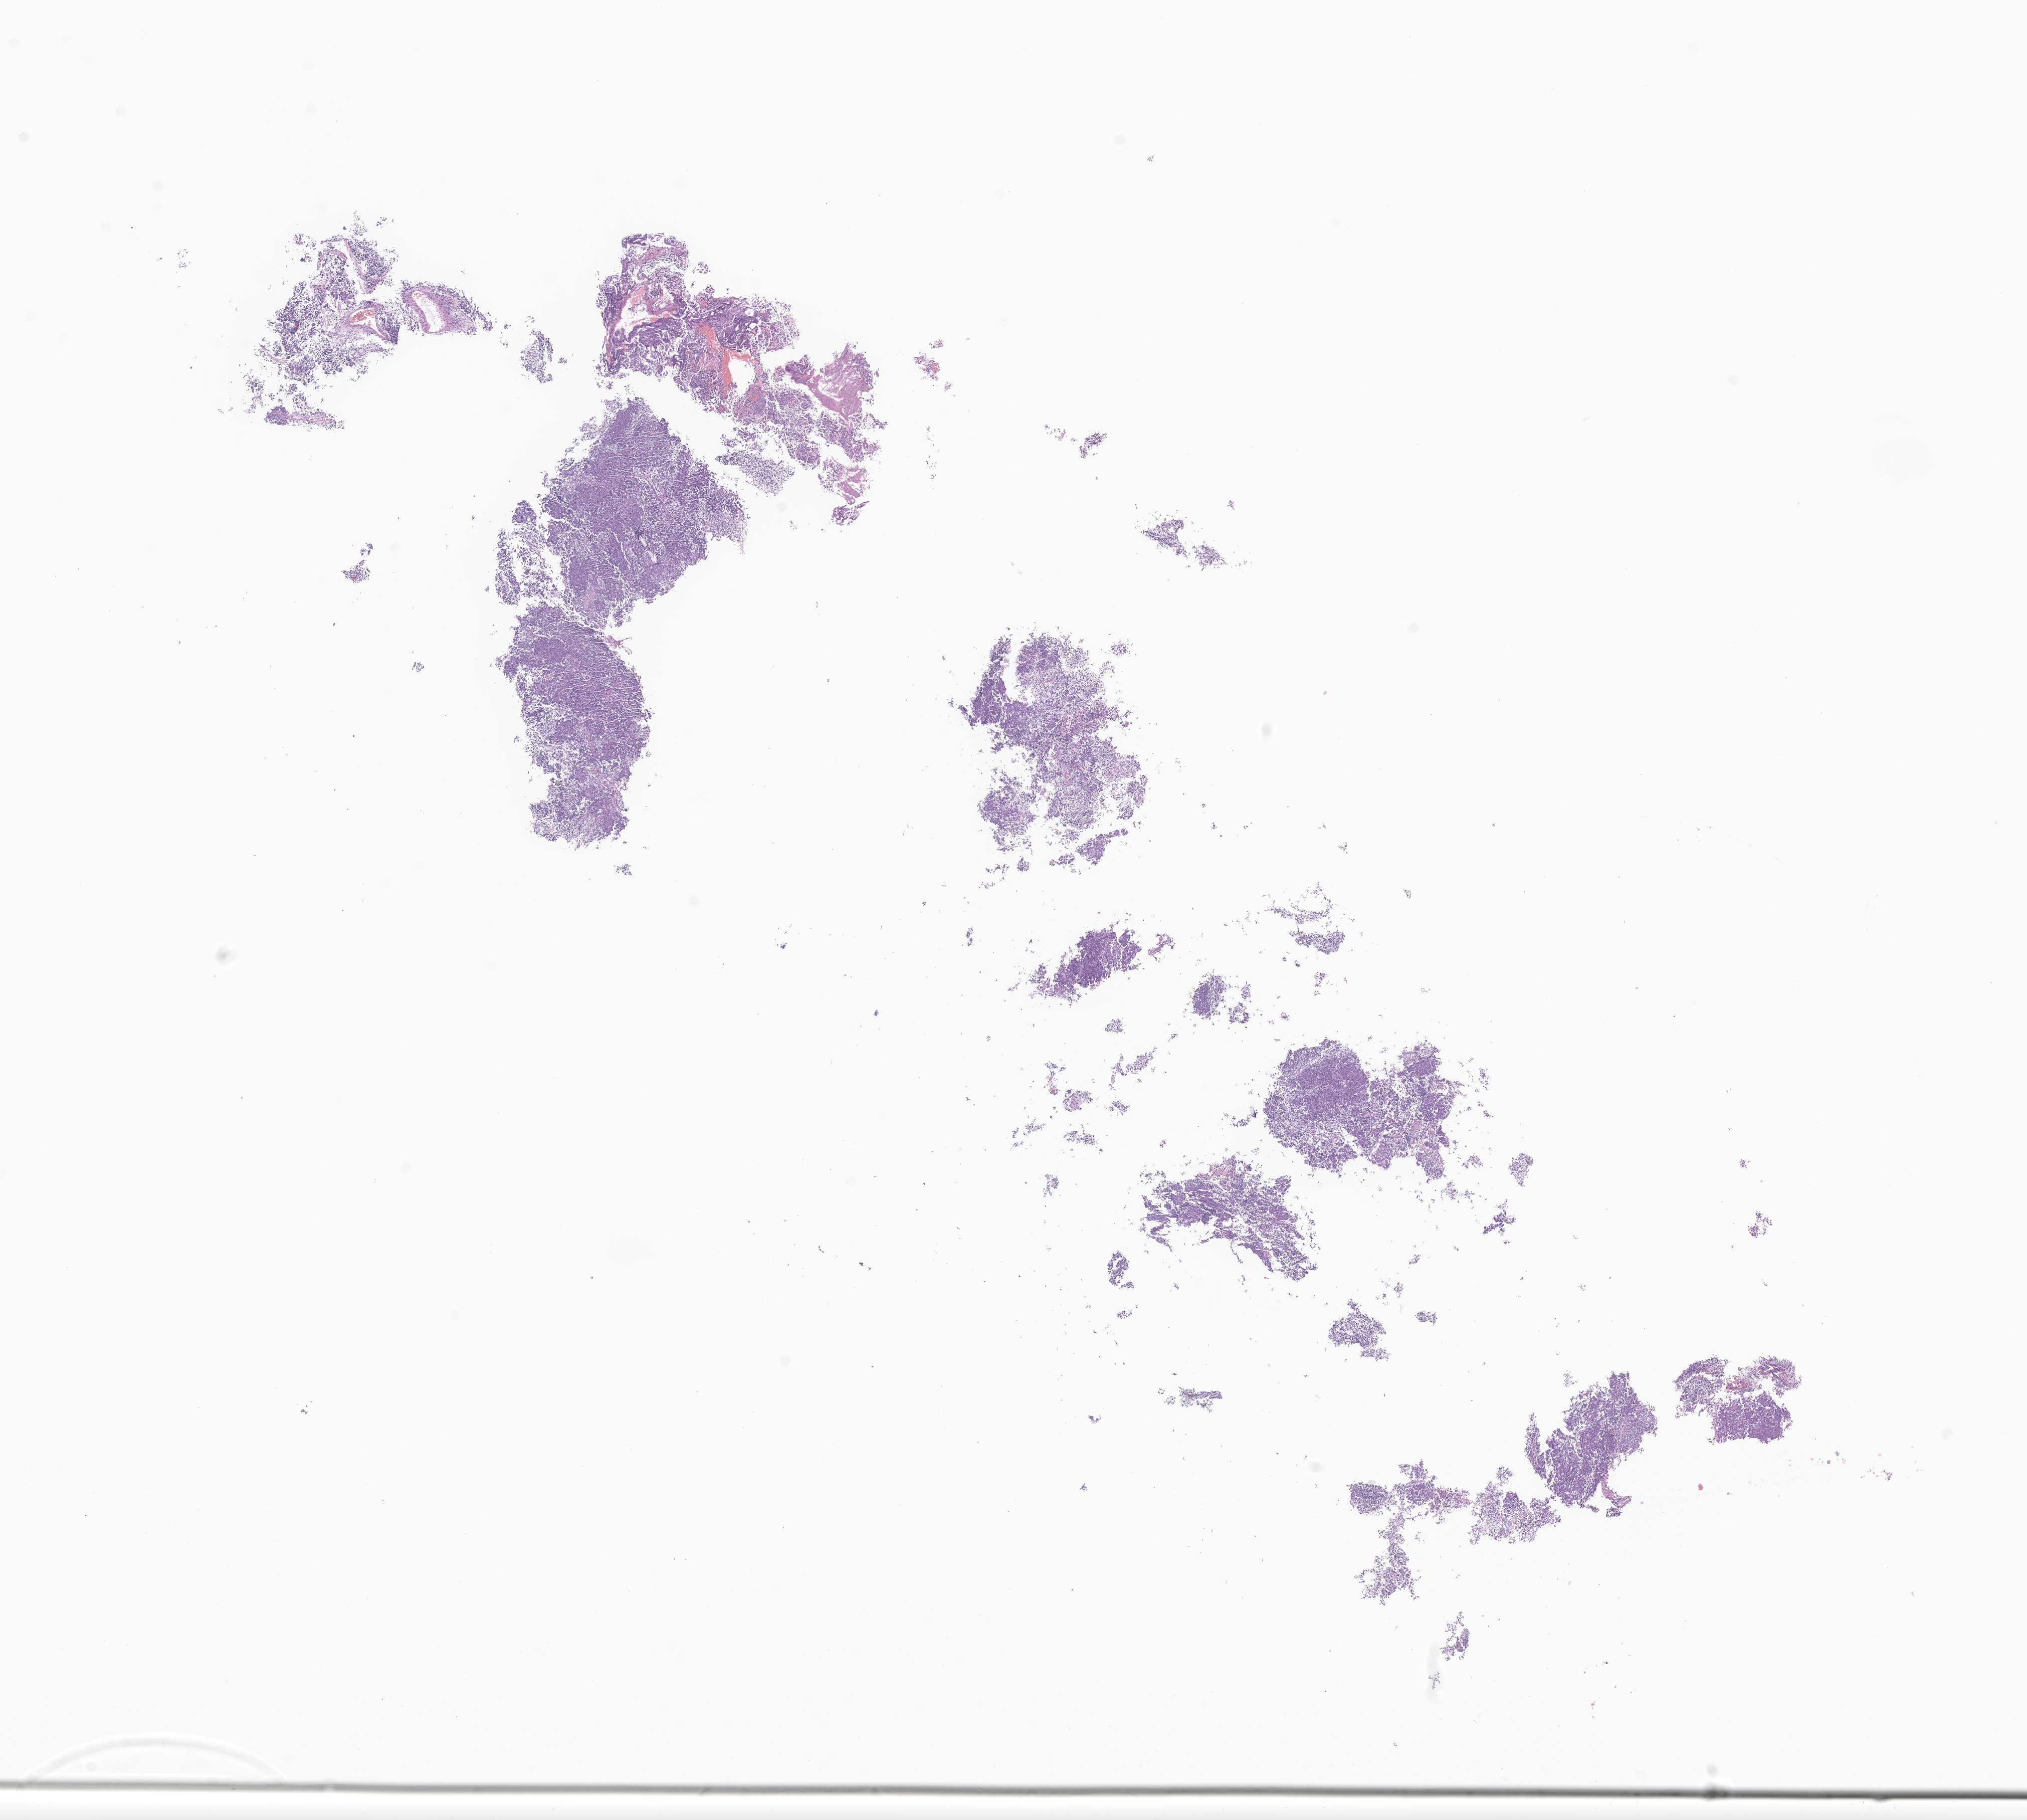
Digitized haematoxylin and eosin-stained section of tumor tissue from the brain, shown as a low-resolution overview of the whole scanned area (about 17.0 x 15.3 mm), FFPE section. Patient: male, age 158 months.
• diagnosis: Medulloblastoma, NOS